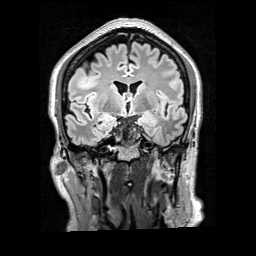
Brain MRI from a brain-tumour surgery series, one coronal slice. Position 109 of 200 along the scan axis. T2 FLAIR. 256 × 256 image matrix, field of view 256 × 256 mm. Case-level facts recorded for this patient, not image findings: histopathology: Glioblastoma; WHO grade: 4; IDH mutation: no; tumour location: Right Frontal.
Annotated regions visible in this slice (outlined manually by an expert reader):
- tumour: bounding box [x1, y1, x2, y2] px = [76, 71, 101, 90]